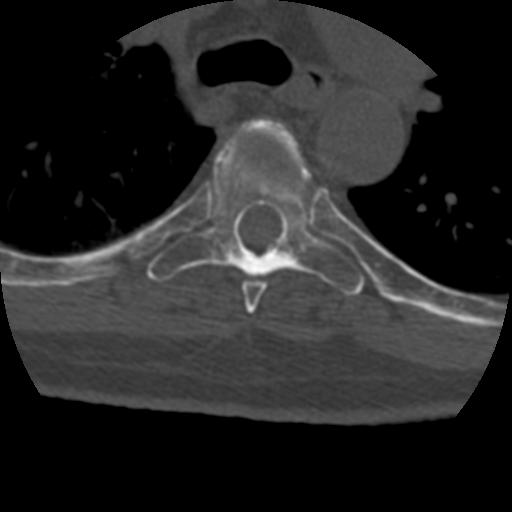
CT including the spine, one axial slice; slice 307 of 399 in the series (ordered by position); bone window (W 1800 / L 400 HU); 1.25 mm slice thickness; 512 × 512 image matrix. Patient age 69 years. From the clinical record (not read from this slice): primary cancer: prostate.
Structures marked on this image (semi-automatically segmented with operator editing):
- T5 vertebra: box from (x=242, y=119) to (x=302, y=314) px
- T6 vertebra: (x=147, y=134)–(x=365, y=296)